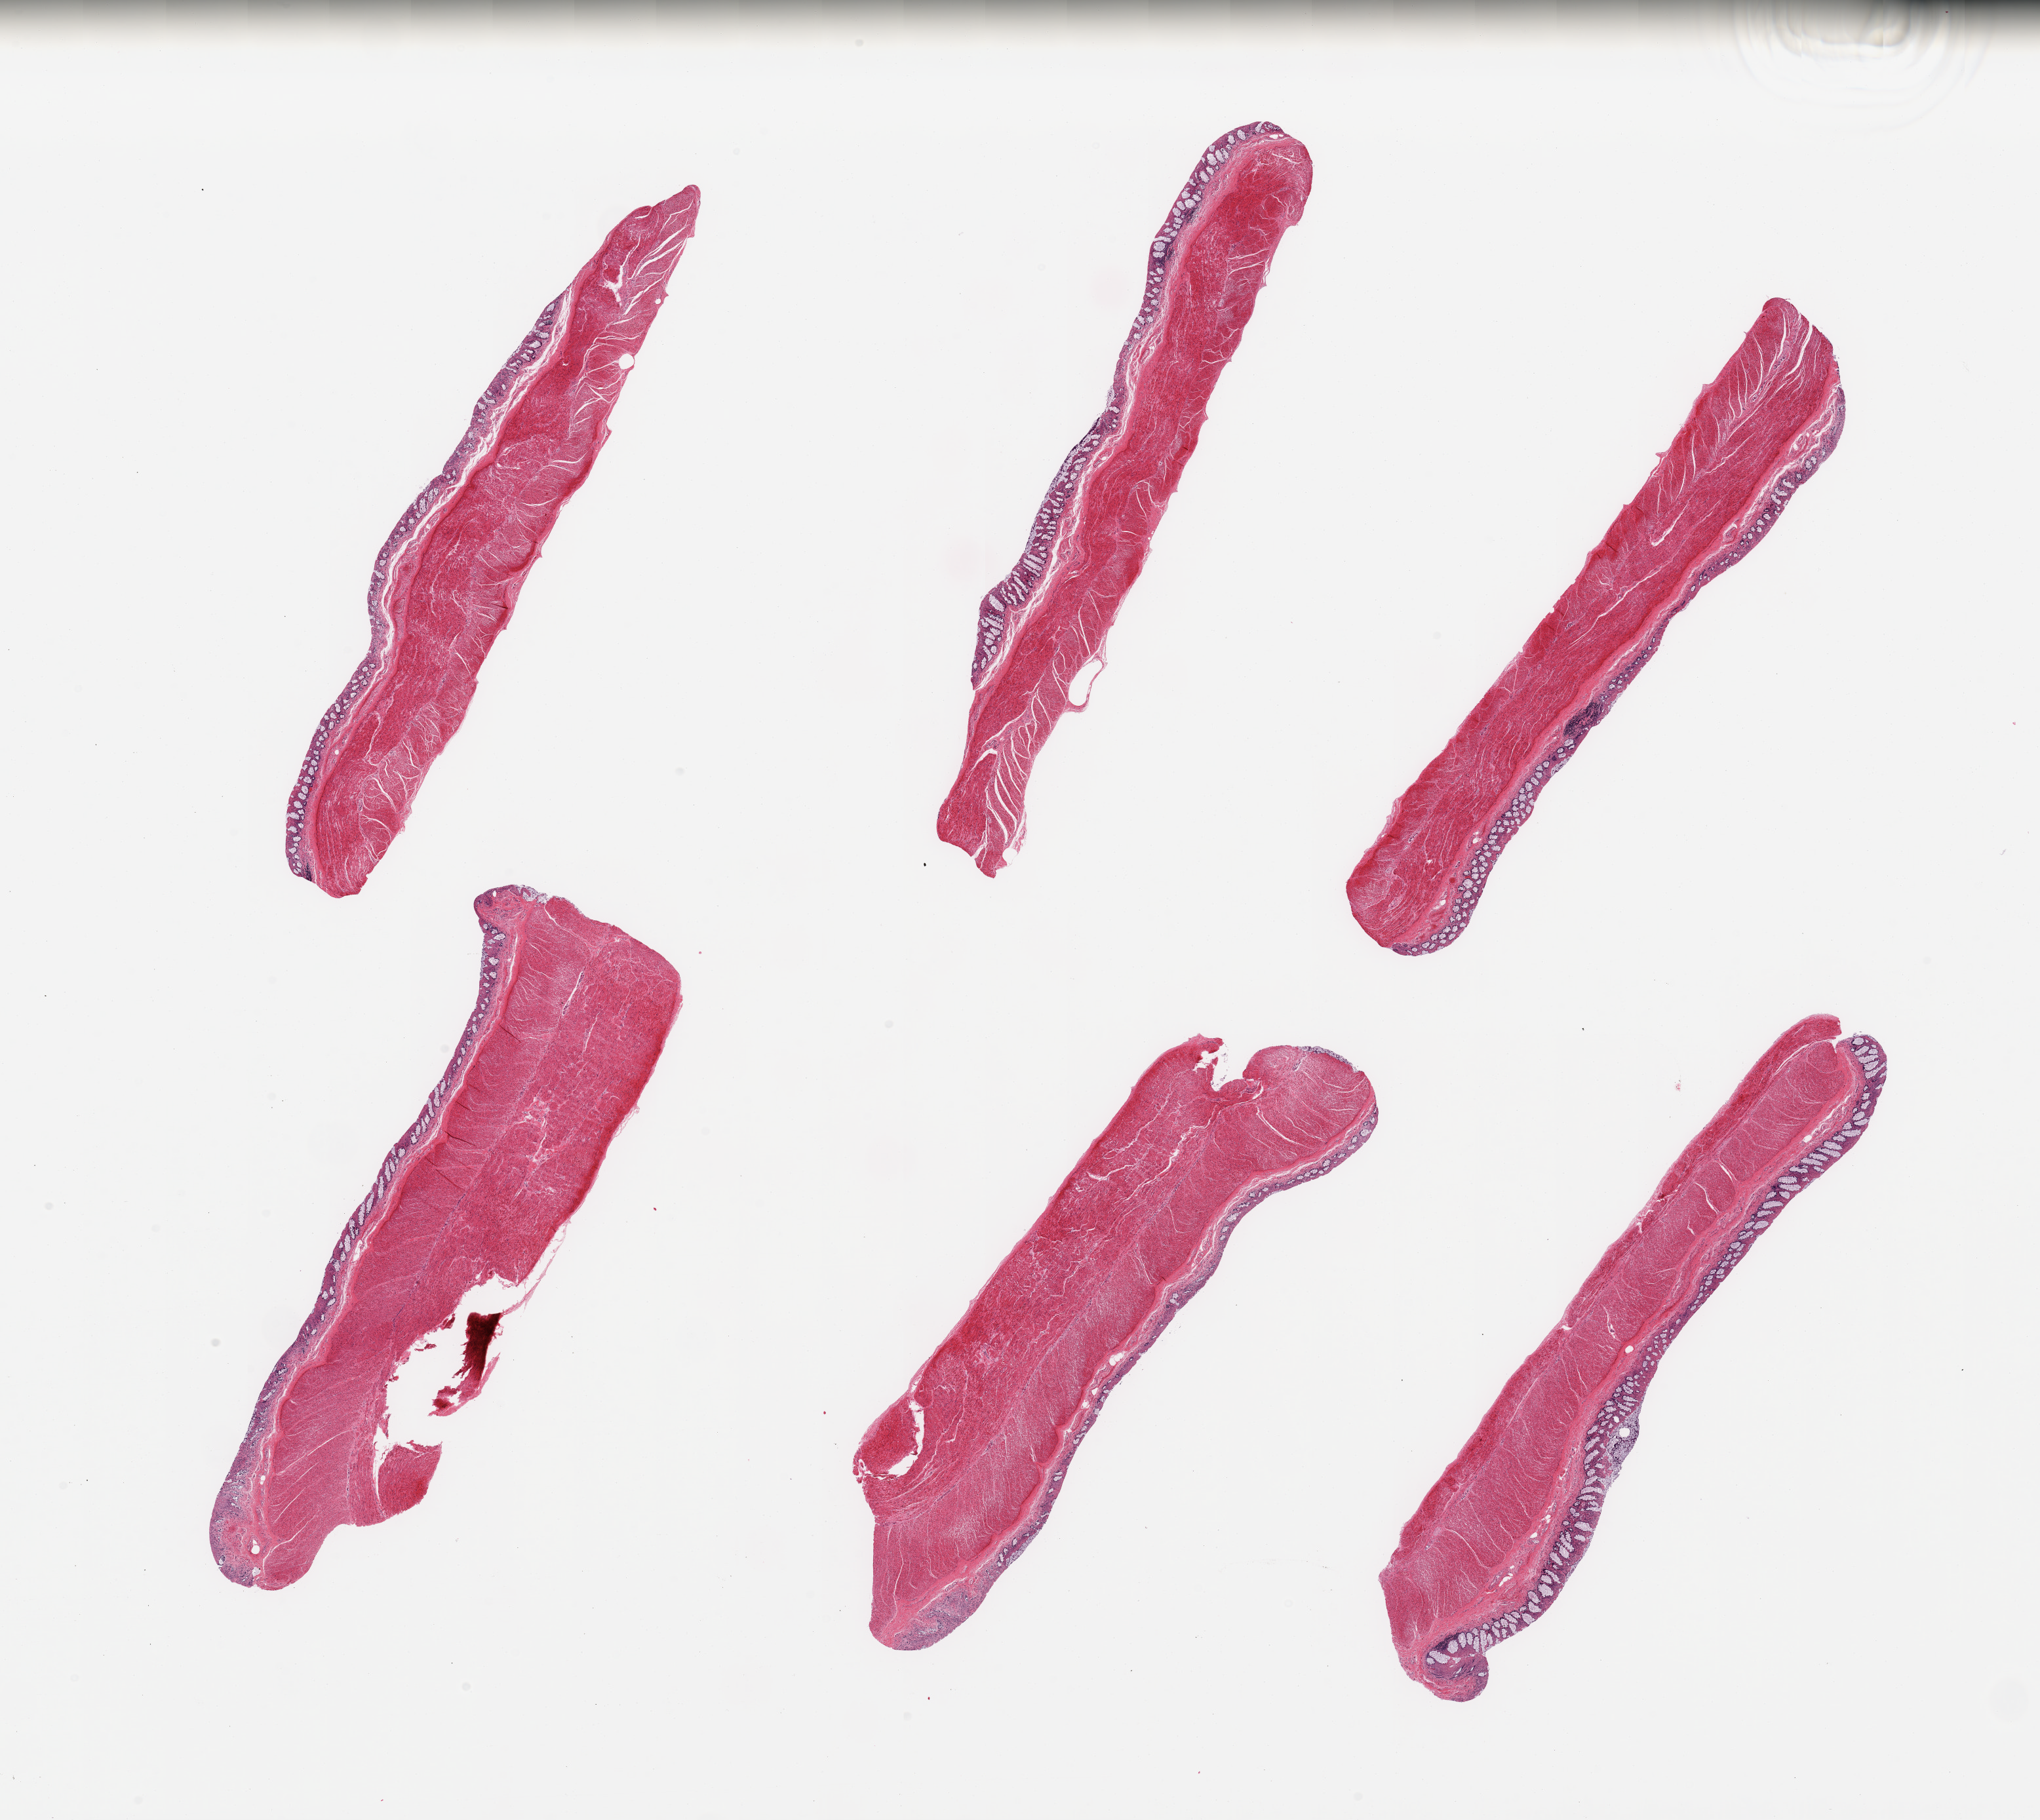
Digitized haematoxylin and eosin-stained section — a low-resolution overview of the entire scanned area, about 24.6 x 22.0 mm (acquisition: 20x scan), PAXgene-fixed, paraffin-embedded tissue, target tissue: sigmoid colon, donor tissue sample. Male donor.
Review note (as recorded): 6 pieces, ~90% target muscularis; ~10% auolyzing contaminant mucosa.